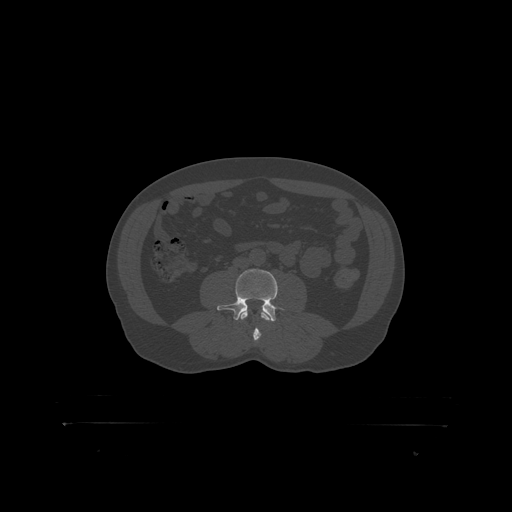
CT including the spine, one axial slice; bone window (W 1800 / L 400 HU); 1.25 mm slice thickness; 512 × 512 image matrix. Patient: male, 46 years. Case-level facts recorded for this patient, not image findings: primary cancer: skin.
Structures marked on this image (semi-automatically segmented with operator editing):
- L3 vertebra: bounding box <241,312,268,319> (left, top, right, bottom; pixels)
- L4 vertebra: <219,269,286,318>